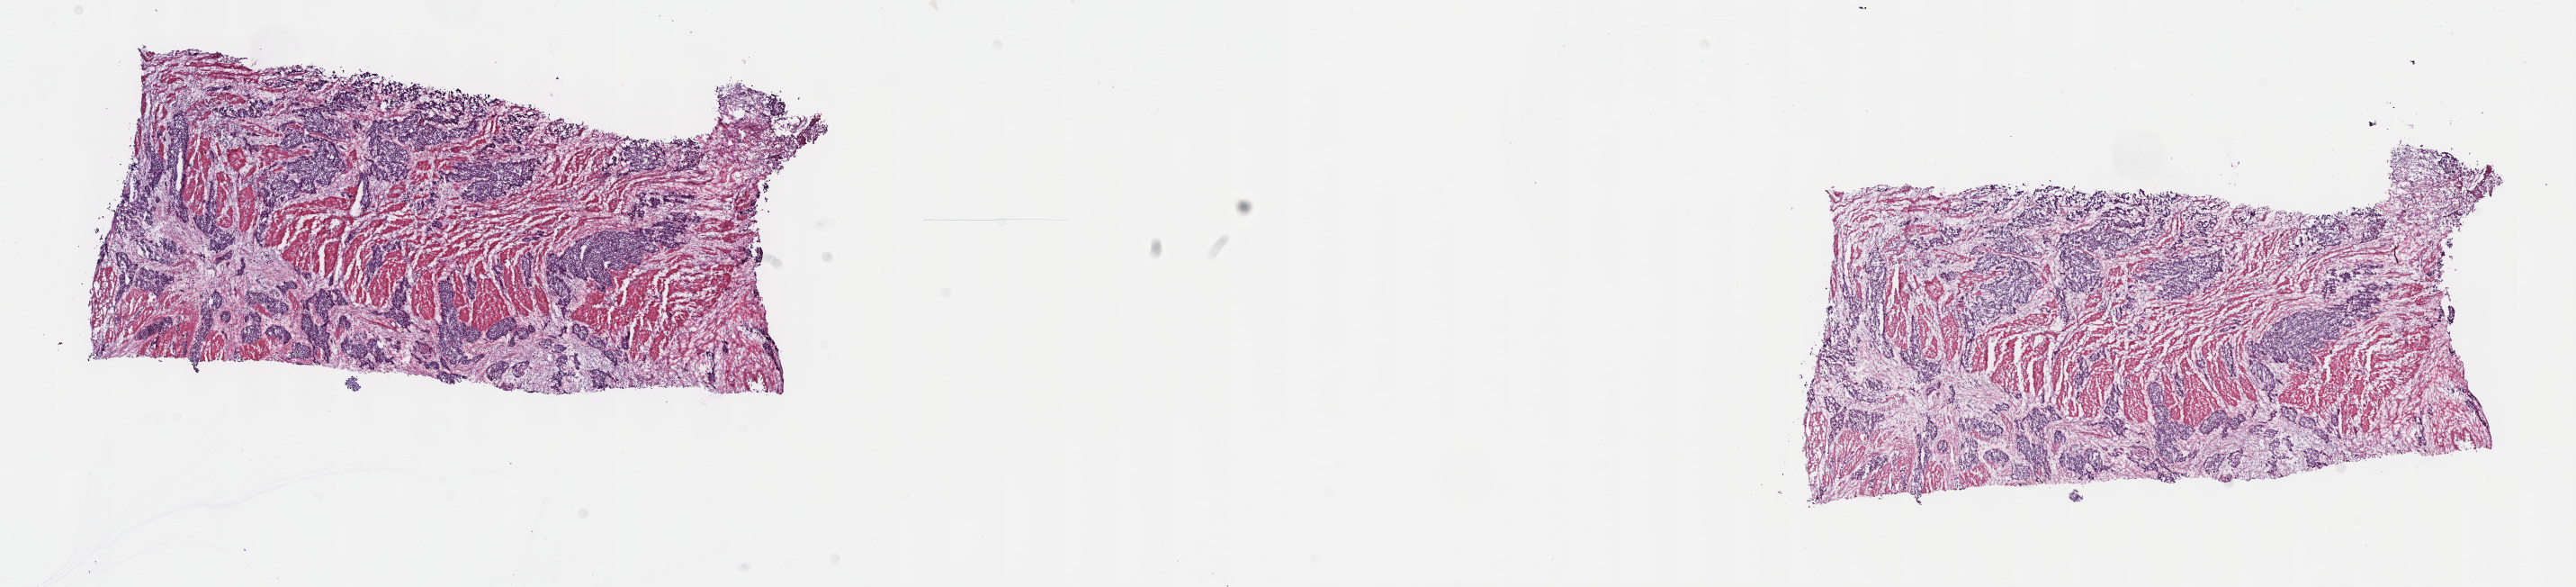
Digitized Hematoxylin and eosin (H&E) stained tissue section (whole slide) — whole scanned area (about 23.2 x 5.3 mm, from a 40x scan) shown as a low-resolution overview; frozen section; sample: primary tumour, esophagus. Patient: male, age at initial diagnosis 62 years. Histologic grade: G3 (poorly differentiated). Pathologist review of this section (percent, as recorded): tumour cells 65%, tumour nuclei 65%, normal cells 0%, stromal cells 35%, necrosis 0%. Inflammatory infiltration, as recorded: lymphocyte infiltration 5%, monocyte infiltration 0%, neutrophil infiltration 0%.
Histologic diagnosis: Squamous cell carcinoma, NOS (middle third of esophagus). AJCC pathologic stage: IIA (6th edition).